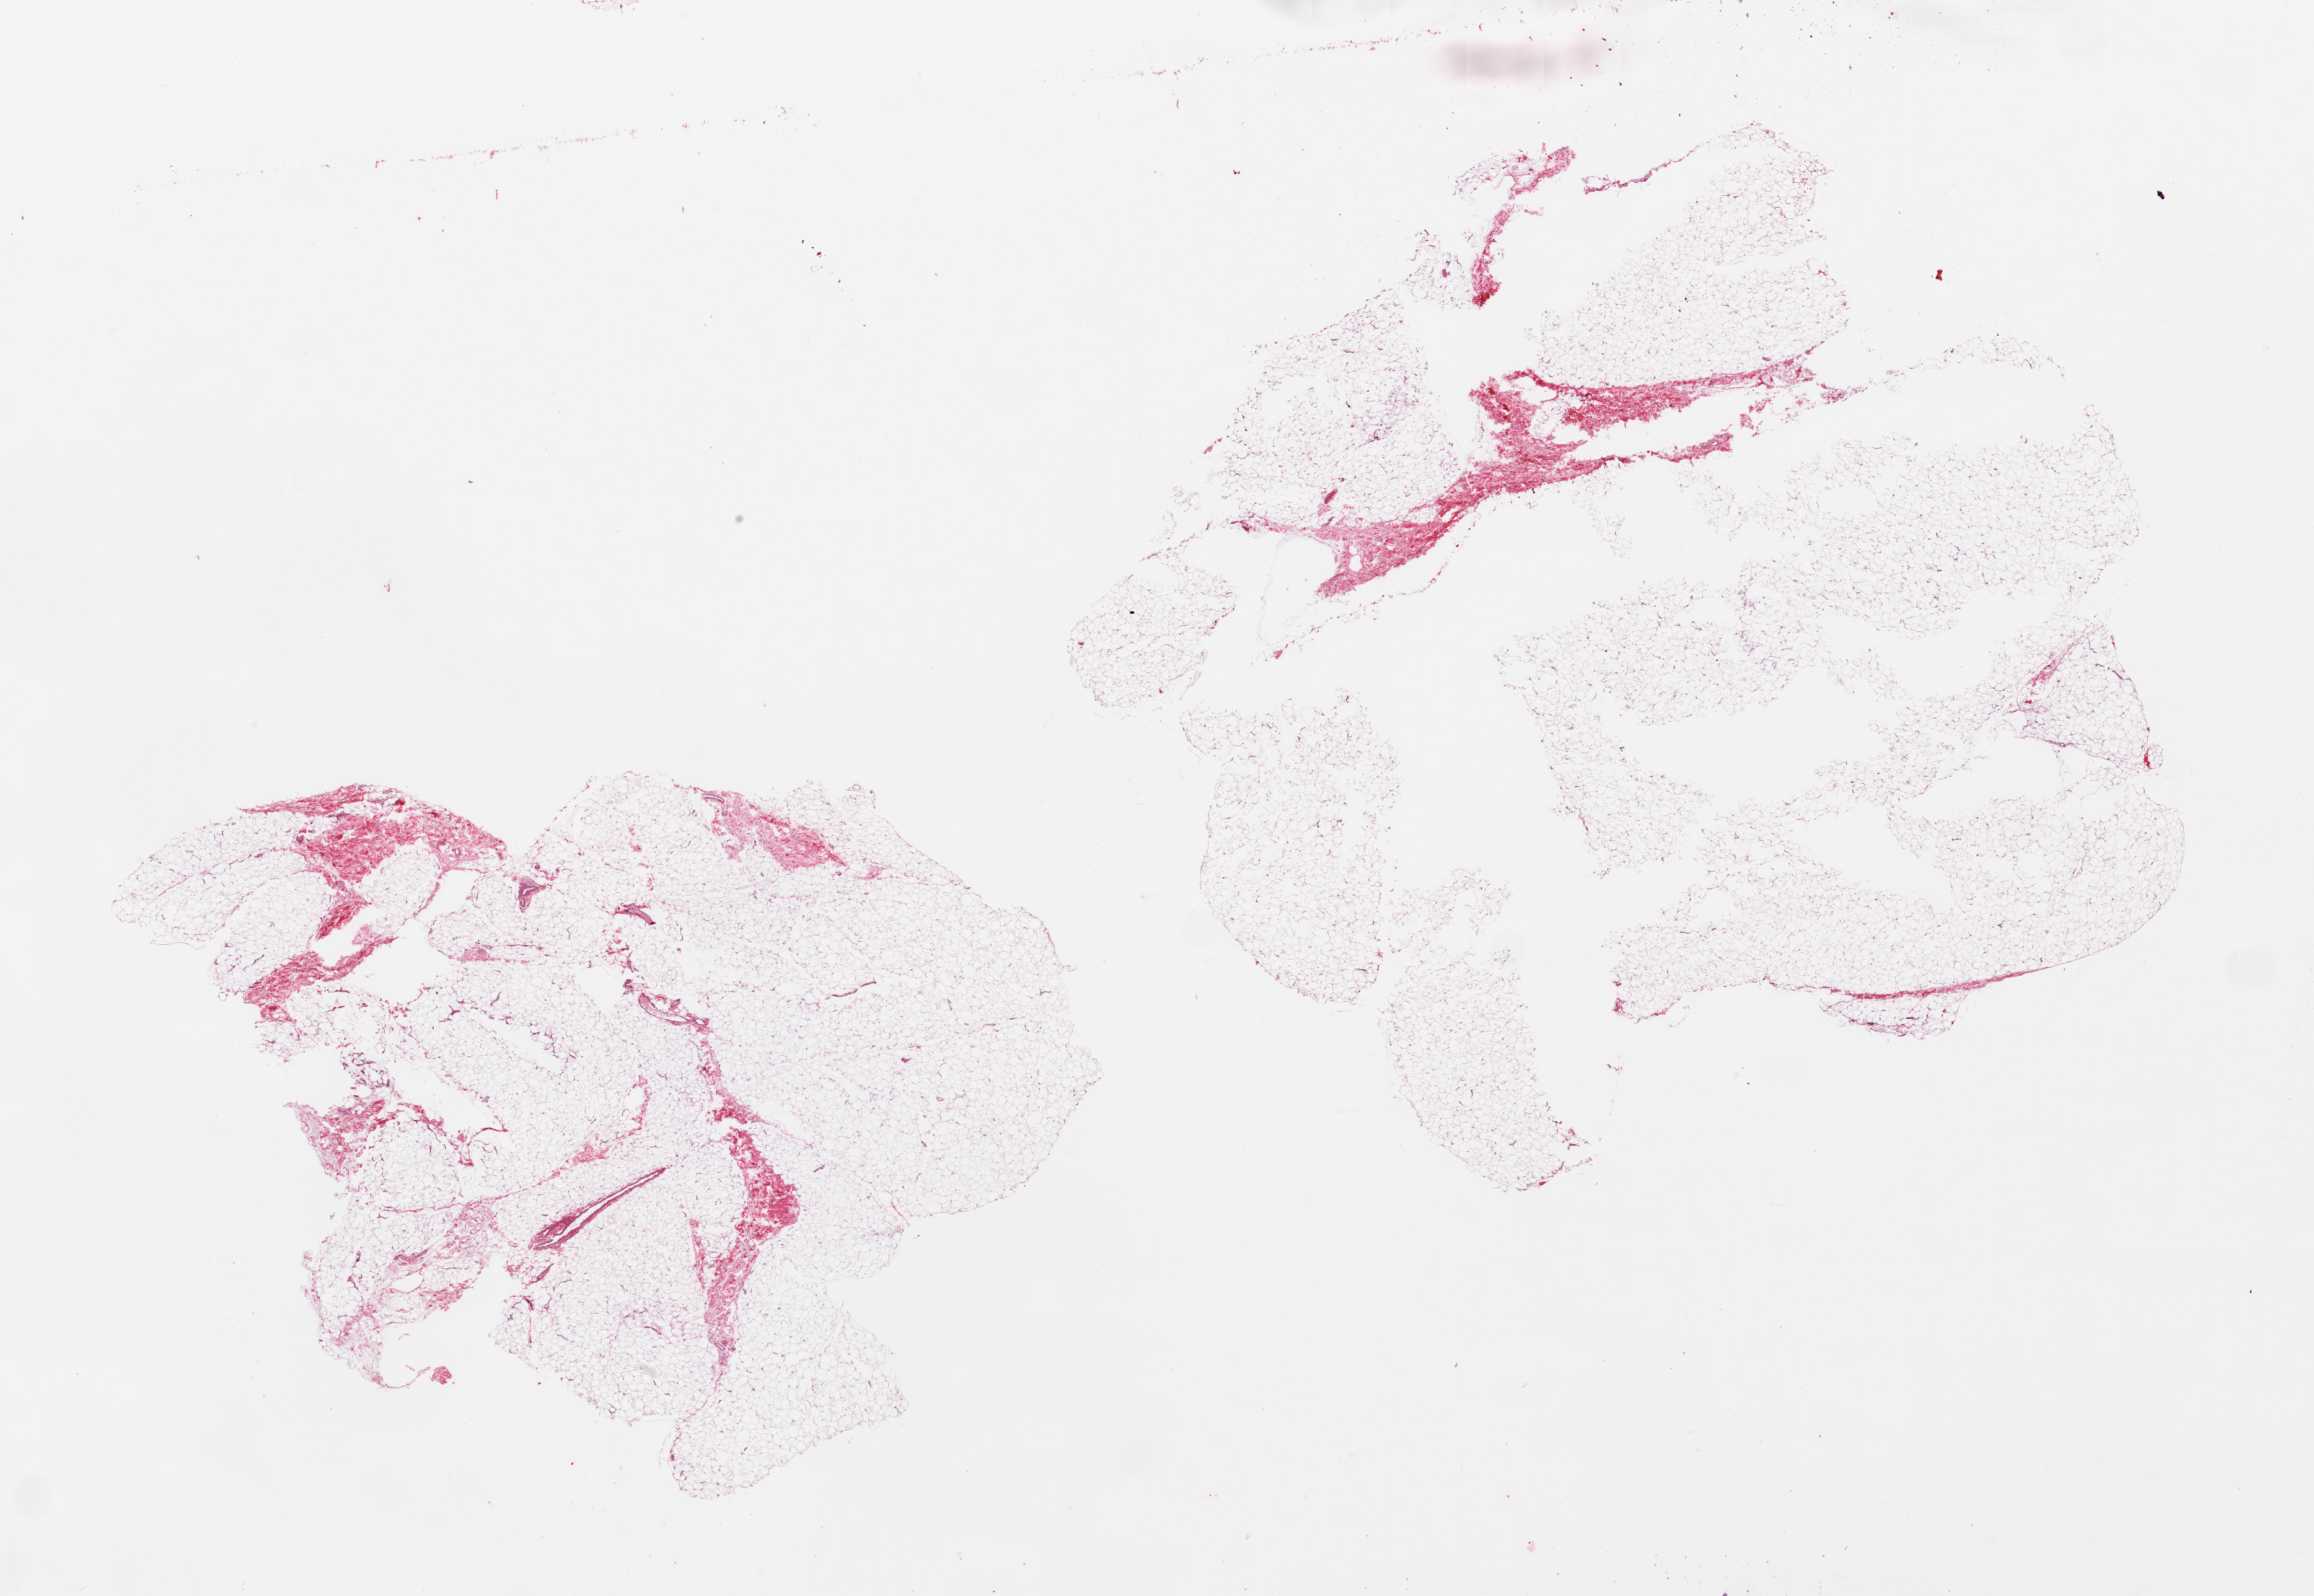
Hematoxylin and eosin (H&E) whole-slide image, brightfield — low-resolution overview of the scanned area, about 29.5 x 20.4 mm (slide scanned at 20x), PAXgene-fixed, paraffin-embedded tissue, section of adipose tissue (target tissue), donor tissue sample. Donor sex: male.
- pathologist's review note for this sample: 2 pieces; adipose tissue with ~10% fibrous component, some tissue defects